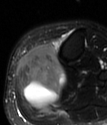
MRI of an extremity soft-tissue mass, one axial slice; position 28 of 78 along the scan axis; T2-weighted fat-saturated; MR volume resampled by the dataset authors to the PET/CT grid (not the native acquisition matrix); 3.27 mm slice thickness; 107 × 125 image matrix, field of view 104 × 122 mm. Female patient. From the clinical record (not read from this slice): histological type: extraskeletal high grade osteogenic sarcoma; grade: high; site of the primary tumour: left calf.
Outlined on this slice (expert contour drawn on MRI and transferred to this co-registered scan by the dataset authors):
- gross tumour volume (mass): bounding box <16,45,65,106> (left, top, right, bottom; pixels)